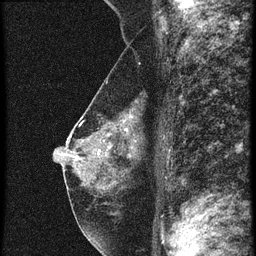
Breast MRI (dynamic contrast-enhanced), one sagittal slice; position 14 of 28 along the scan axis; 6 images stored at this slice position (order not interpretable as contrast timing); 1.5 T; TE 4.2 ms, TR 20.4 ms; 2.3 mm slice thickness; 256 × 256 image matrix, field of view 180 × 180 mm. Patient: female, 46 years. From the clinical record (not read from this slice): setting: breast cancer imaged before/during neoadjuvant chemotherapy; receptor status: triple-negative.
Annotated regions visible in this slice (semi-automatic segmentation, software-assisted and operator-edited):
- analysis volume of interest (the breast-tissue region the enhancement analysis was run in; not a lesion): box from (x=68, y=92) to (x=144, y=195) px
- tumour enhancement mask (voxels above the 90 % enhancement threshold inside the analysis volume of interest): (x=124, y=128)–(x=133, y=149)